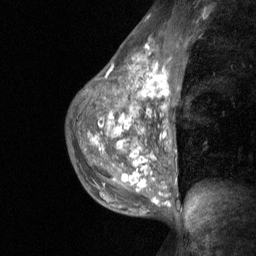
Breast MRI (dynamic contrast-enhanced), one sagittal slice; position 38 of 64 along the scan axis; dynamic contrast-enhanced study with each time point stored as its own series, time point 2 of 3 at this slice position (early post-contrast, ordered by acquisition time); 1.5 T; TE 4.8 ms, TR 27 ms; 256 × 256 image matrix, field of view 200 × 200 mm. Patient: female, 36 years. Case-level facts recorded for this patient, not image findings: setting: breast cancer imaged before/during neoadjuvant chemotherapy; receptor status: HR-positive, HER2-negative.
Structures marked on this image (semi-automatically segmented with operator editing):
- analysis volume of interest (the breast-tissue region the enhancement analysis was run in; not a lesion): bounding box (x1, y1, x2, y2) in pixels: (73, 45, 180, 210)
- tumour enhancement mask (voxels above the 90 % enhancement threshold inside the analysis volume of interest): (92, 77, 165, 204)